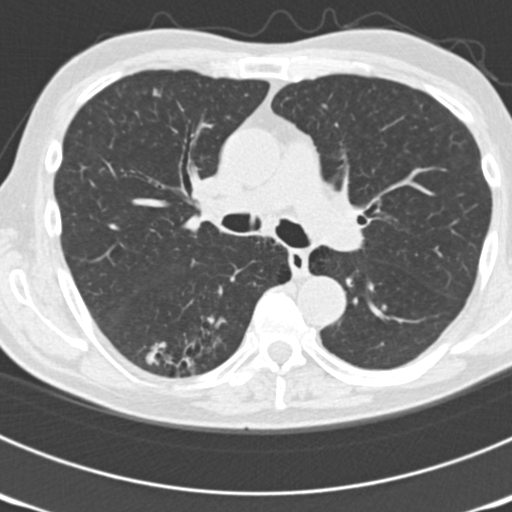
Chest CT (low-dose screening protocol), one axial image. Third annual screen. Lung window (W 1500 / L -600 HU). 2 mm slice thickness. 512 × 512 image matrix. Male participant, aged 70 years at enrolment. Current smoker at enrolment.
- Lesion marked by an expert reader, bounding box [x1, y1, x2, y2] px = [142, 312, 236, 386].
- The screening reader recorded 3 non-calcified nodules or masses ≥4 mm on this exam (right upper lobe, left upper lobe, right lower lobe); which of them this box marks is not recorded.
- Participant outcome: lung cancer diagnosed 14 days after this screen — bronchiolo-alveolar adenocarcinoma, NOS, right lower lobe, poorly differentiated (G3), stage IB (AJCC 6th edition), 30 mm at pathology.